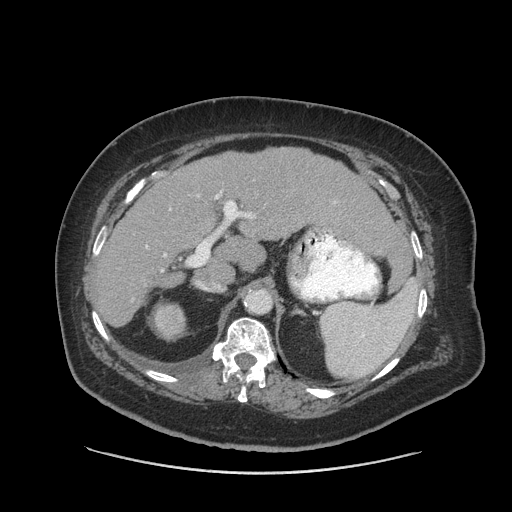
Contrast-enhanced abdominal CT (liver protocol), one axial slice. Position 52 of 91 along the scan axis. 140 kVp. Soft-tissue window (W 400 / L 40 HU). 512 × 512 image matrix. From the clinical record (not read from this slice): diagnosis: hepatocellular carcinoma (patient treated with transarterial chemoembolisation; whether this scan precedes or follows treatment is not stated here); TNM stage (as recorded): Stage-I; Child-Pugh class: A.
Structures marked on this image (semi-automatically segmented with operator editing):
- liver parenchyma outside the tumour (the mass and vessels are separate outlines, so this box may not span the whole liver): bounding box [x1, y1, x2, y2] px = [94, 147, 397, 326]
- liver vessels: [215, 195, 251, 218]